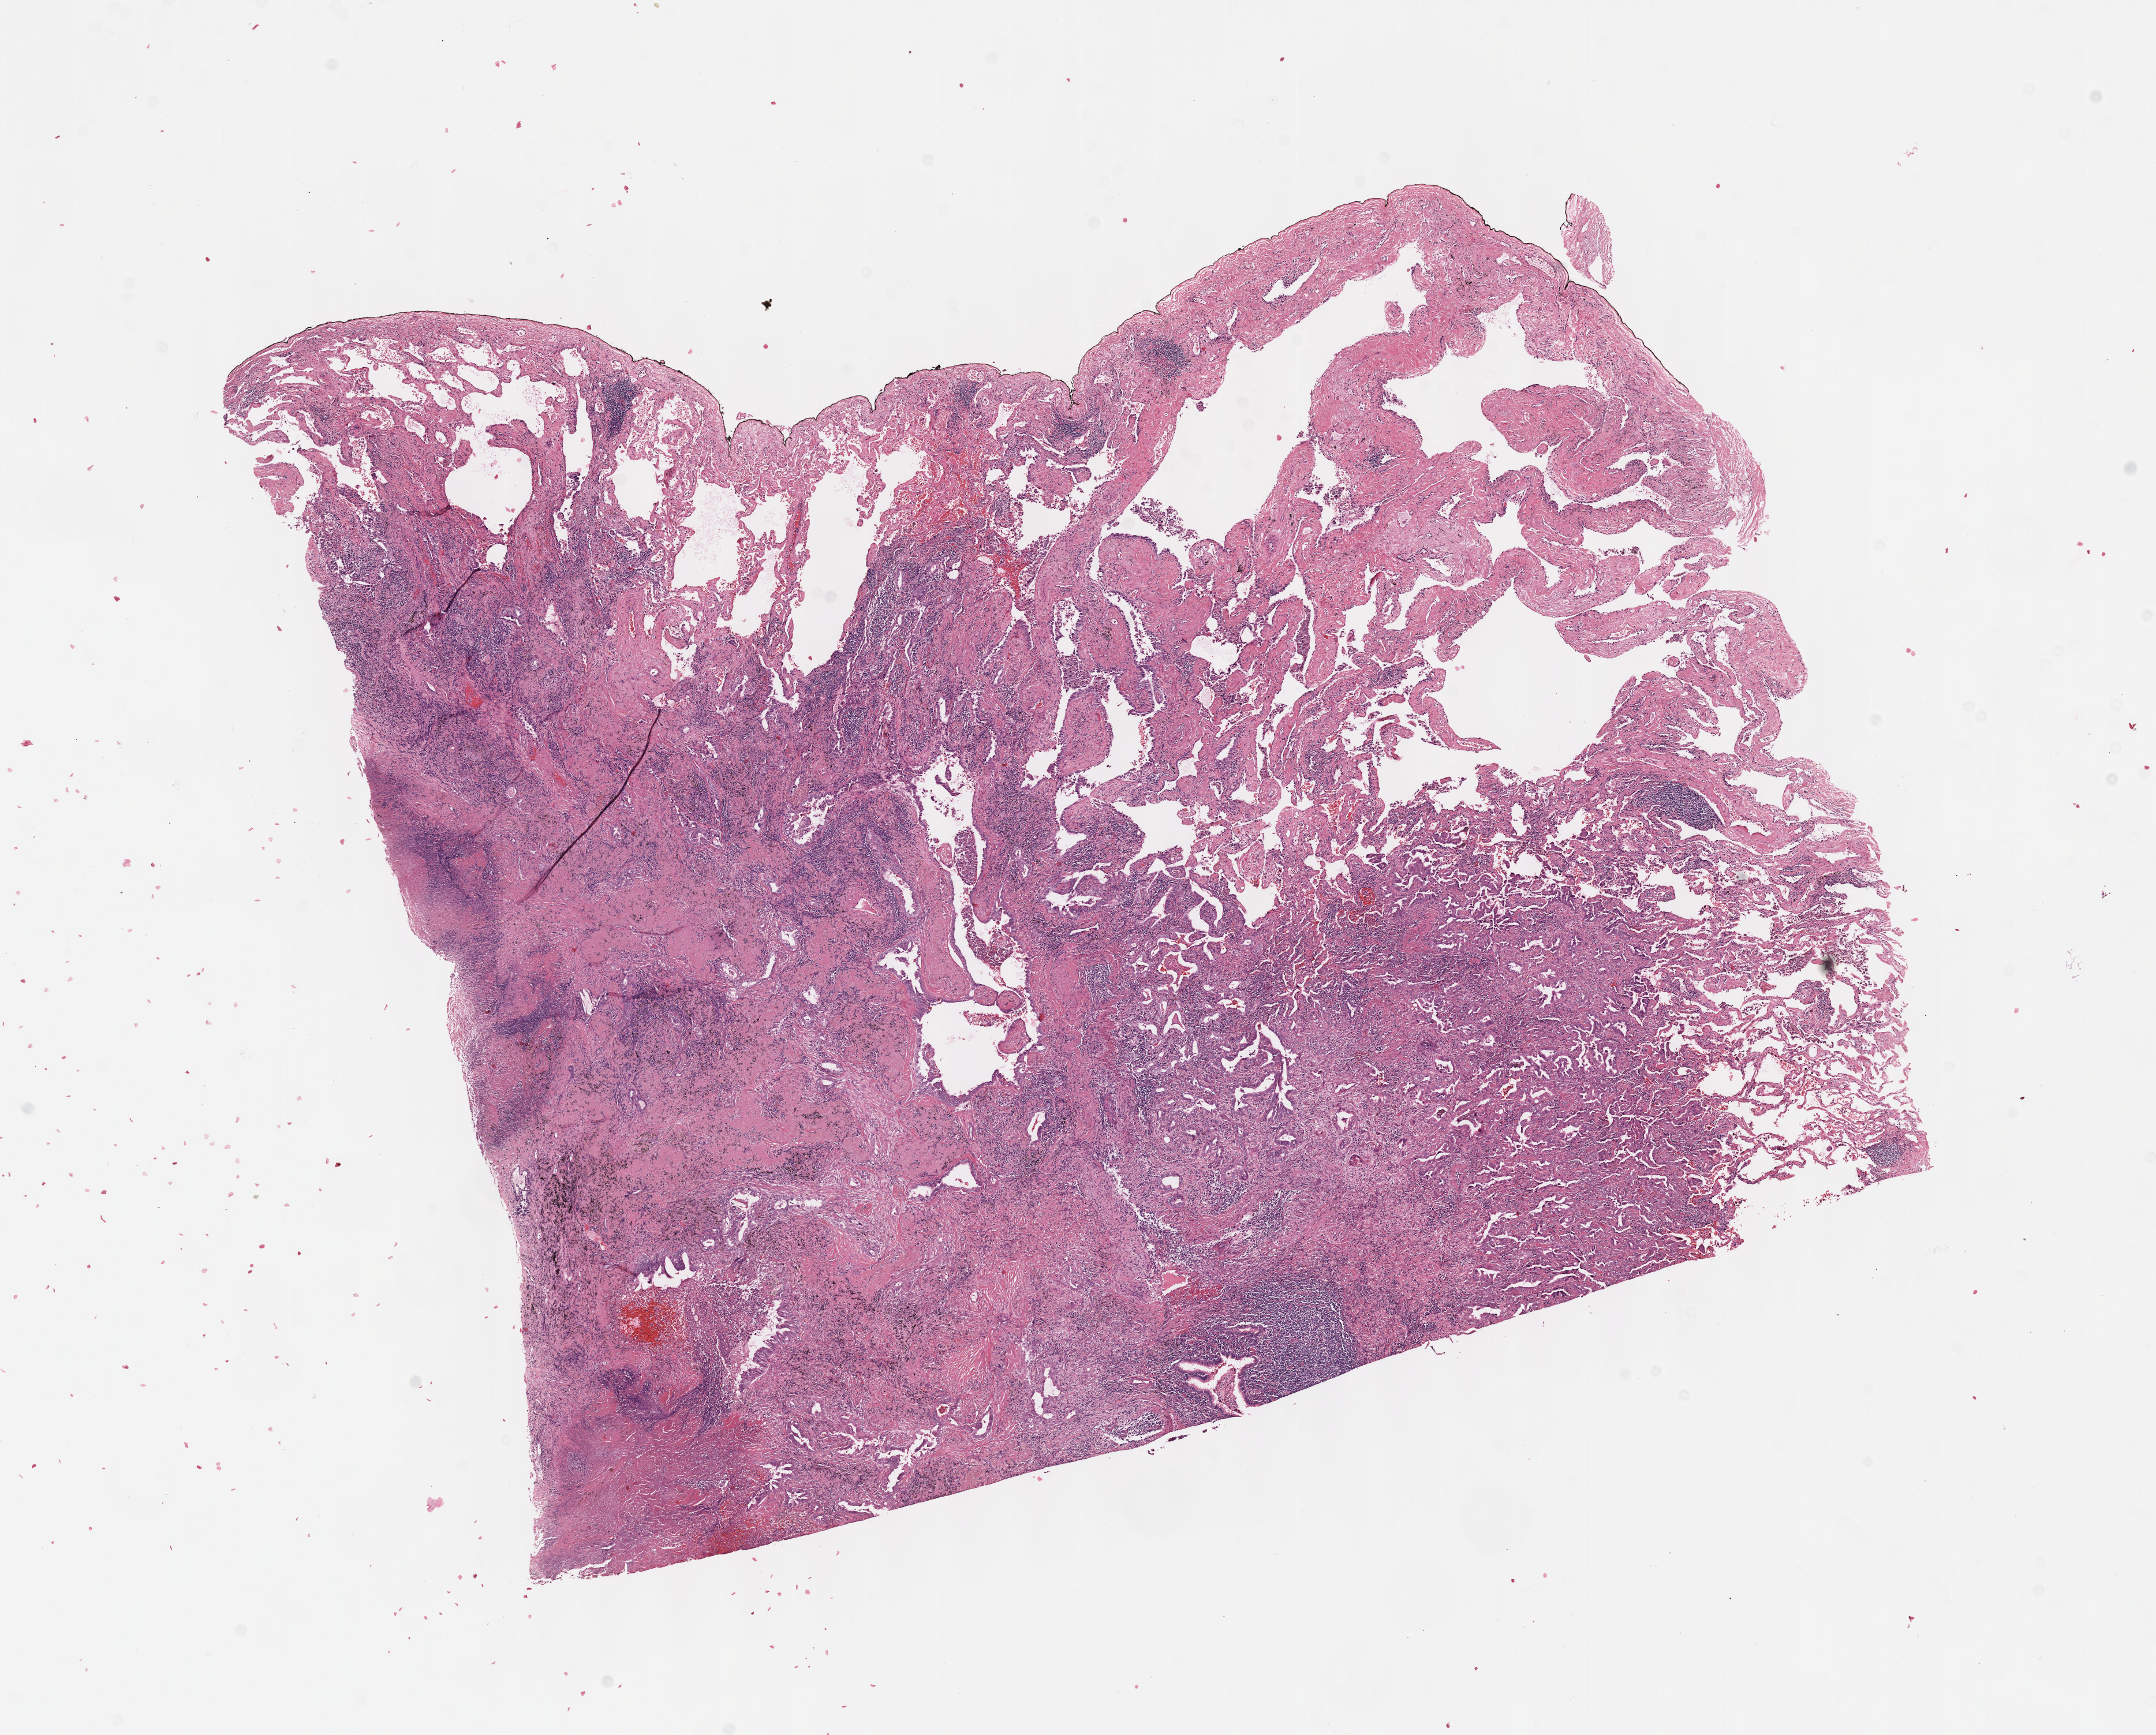
H&E-stained whole-slide image, low-resolution overview of the scanned area, about 15.1 x 12.1 mm (slide scanned at 40x). Formalin-fixed paraffin-embedded (FFPE) diagnostic section. Lung, primary tumour sample. Patient: female, age at initial diagnosis 75 years.
Histologic diagnosis: Adenocarcinoma, NOS.